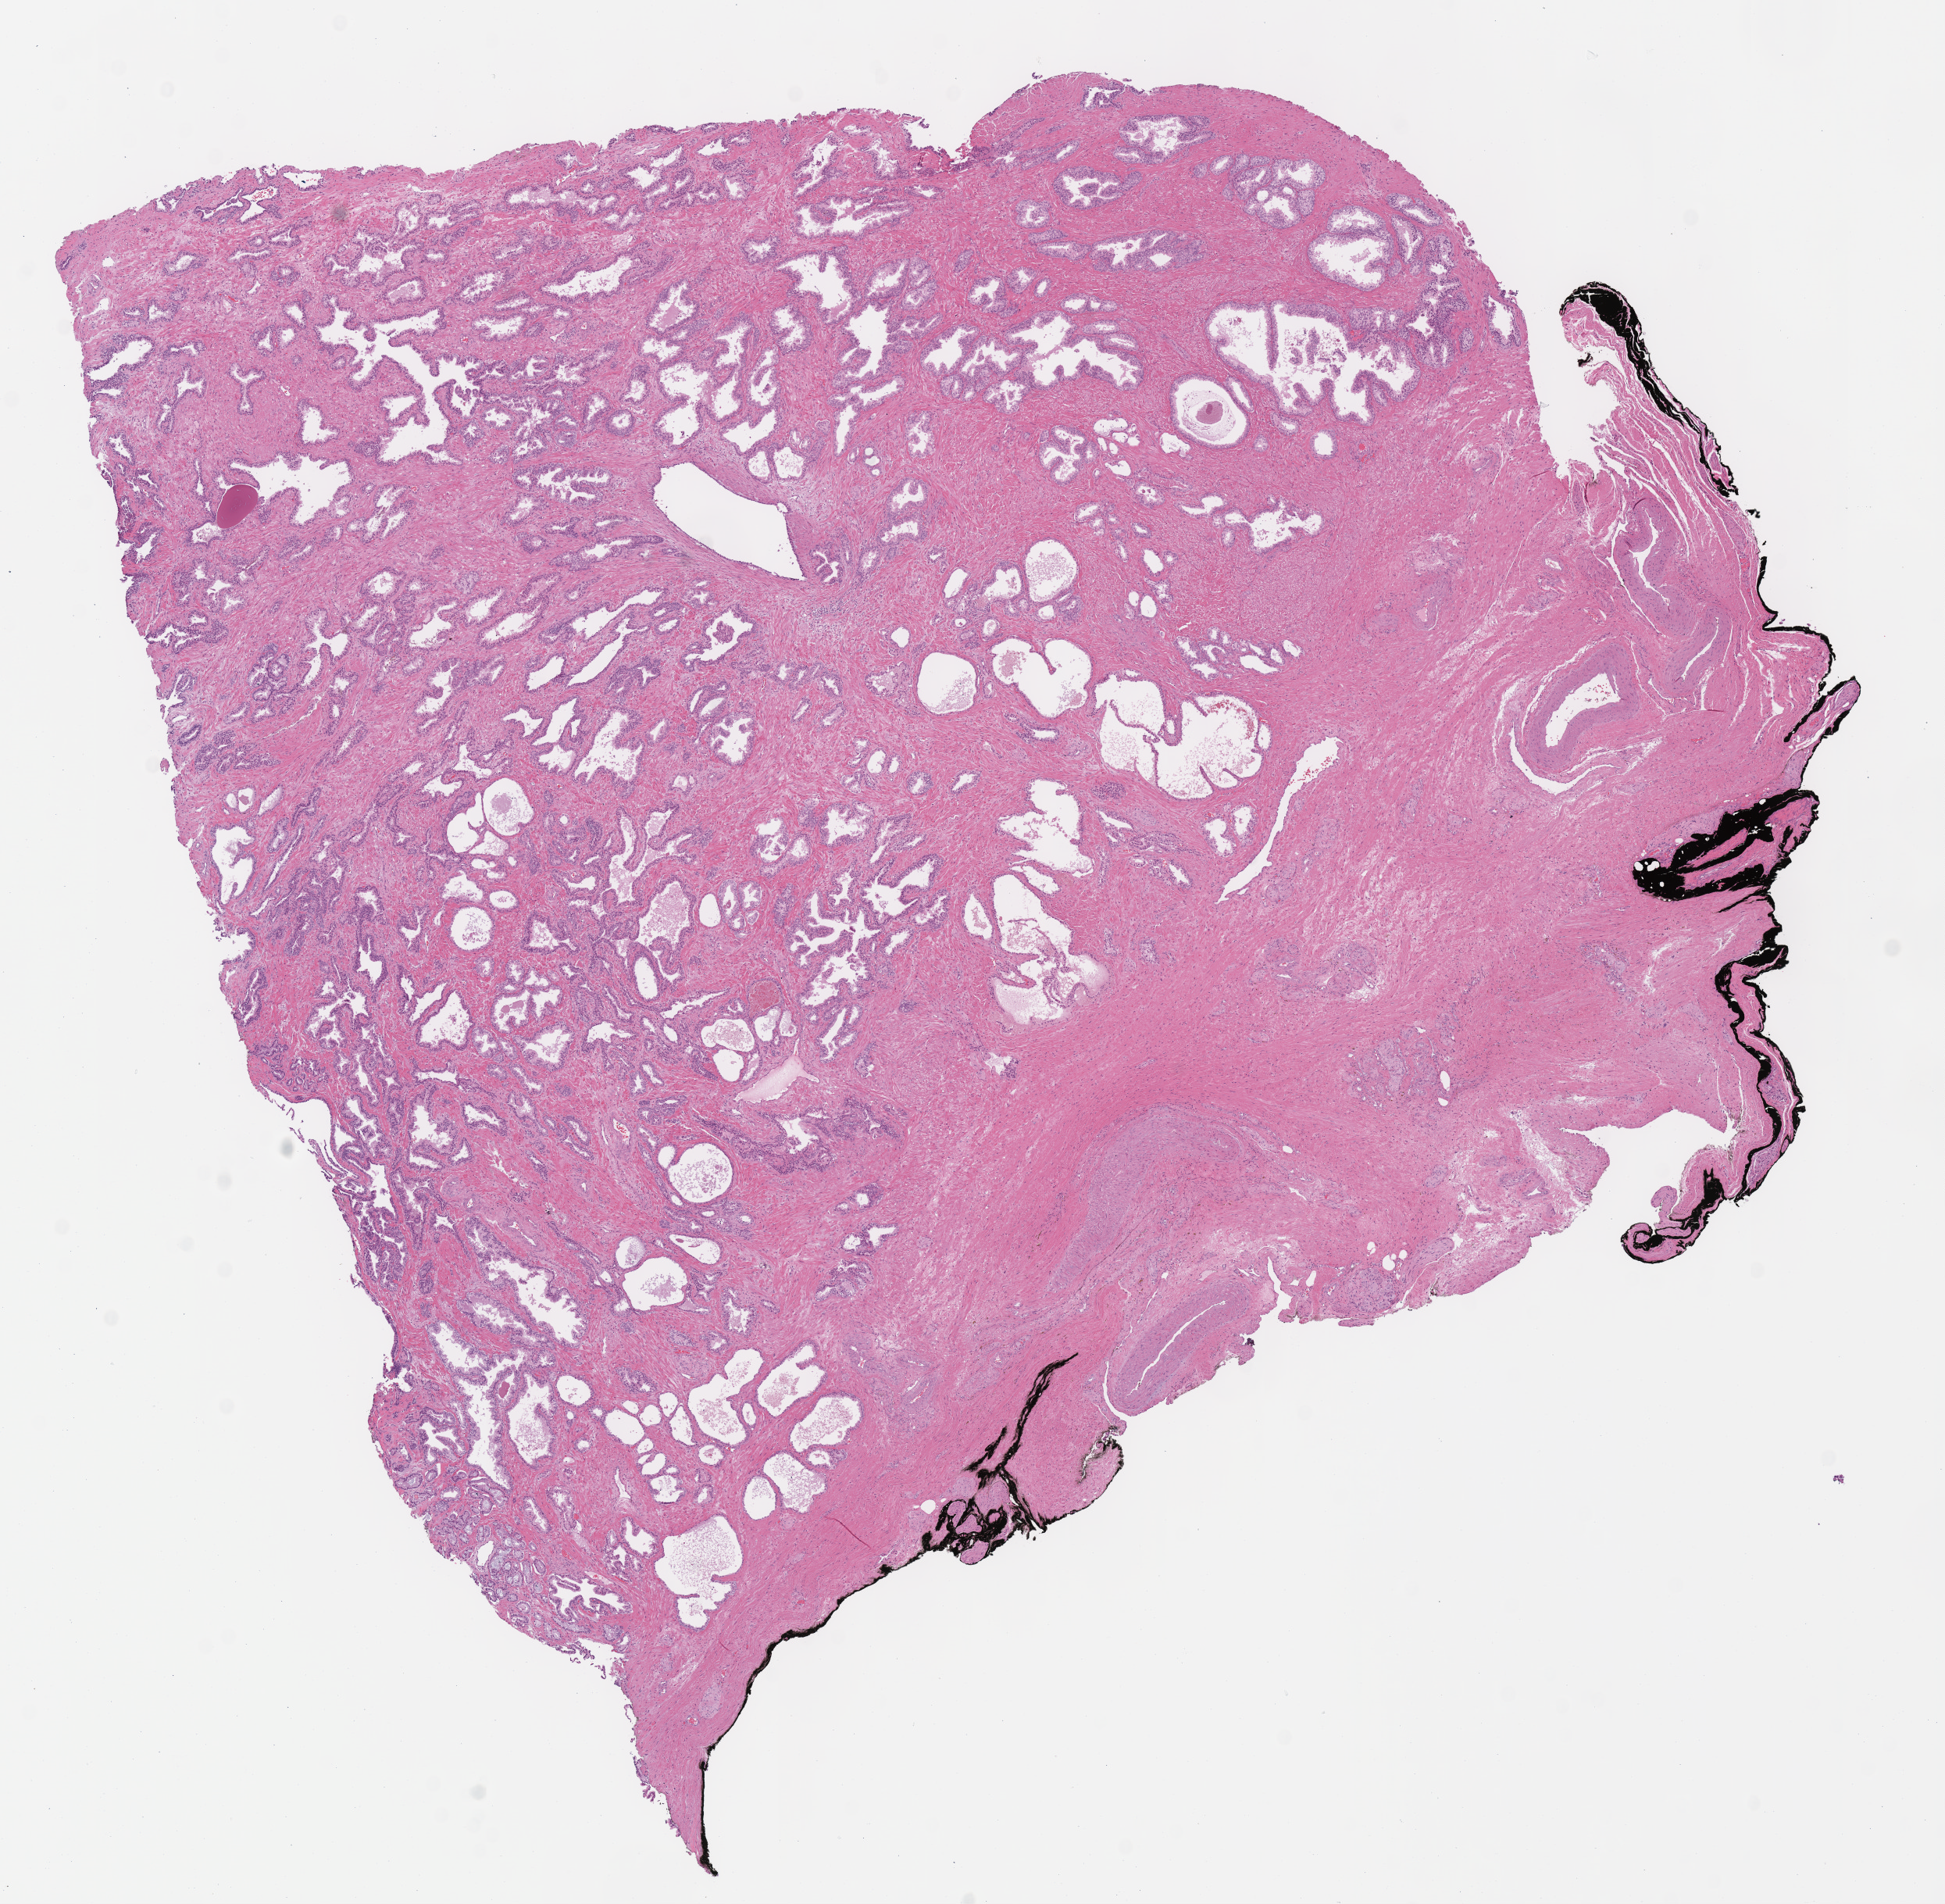
Whole-slide histology image, Hematoxylin and eosin (H&E) stained — whole scanned area (about 9.8 x 9.6 mm, from a 40x scan) shown as a low-resolution overview; formalin-fixed paraffin-embedded (FFPE) diagnostic section; sample: primary tumour, prostate. Male, age 48 years at initial diagnosis. Gleason score: 6 (3+3).
* histologic diagnosis: Acinar cell carcinoma (prostate gland)